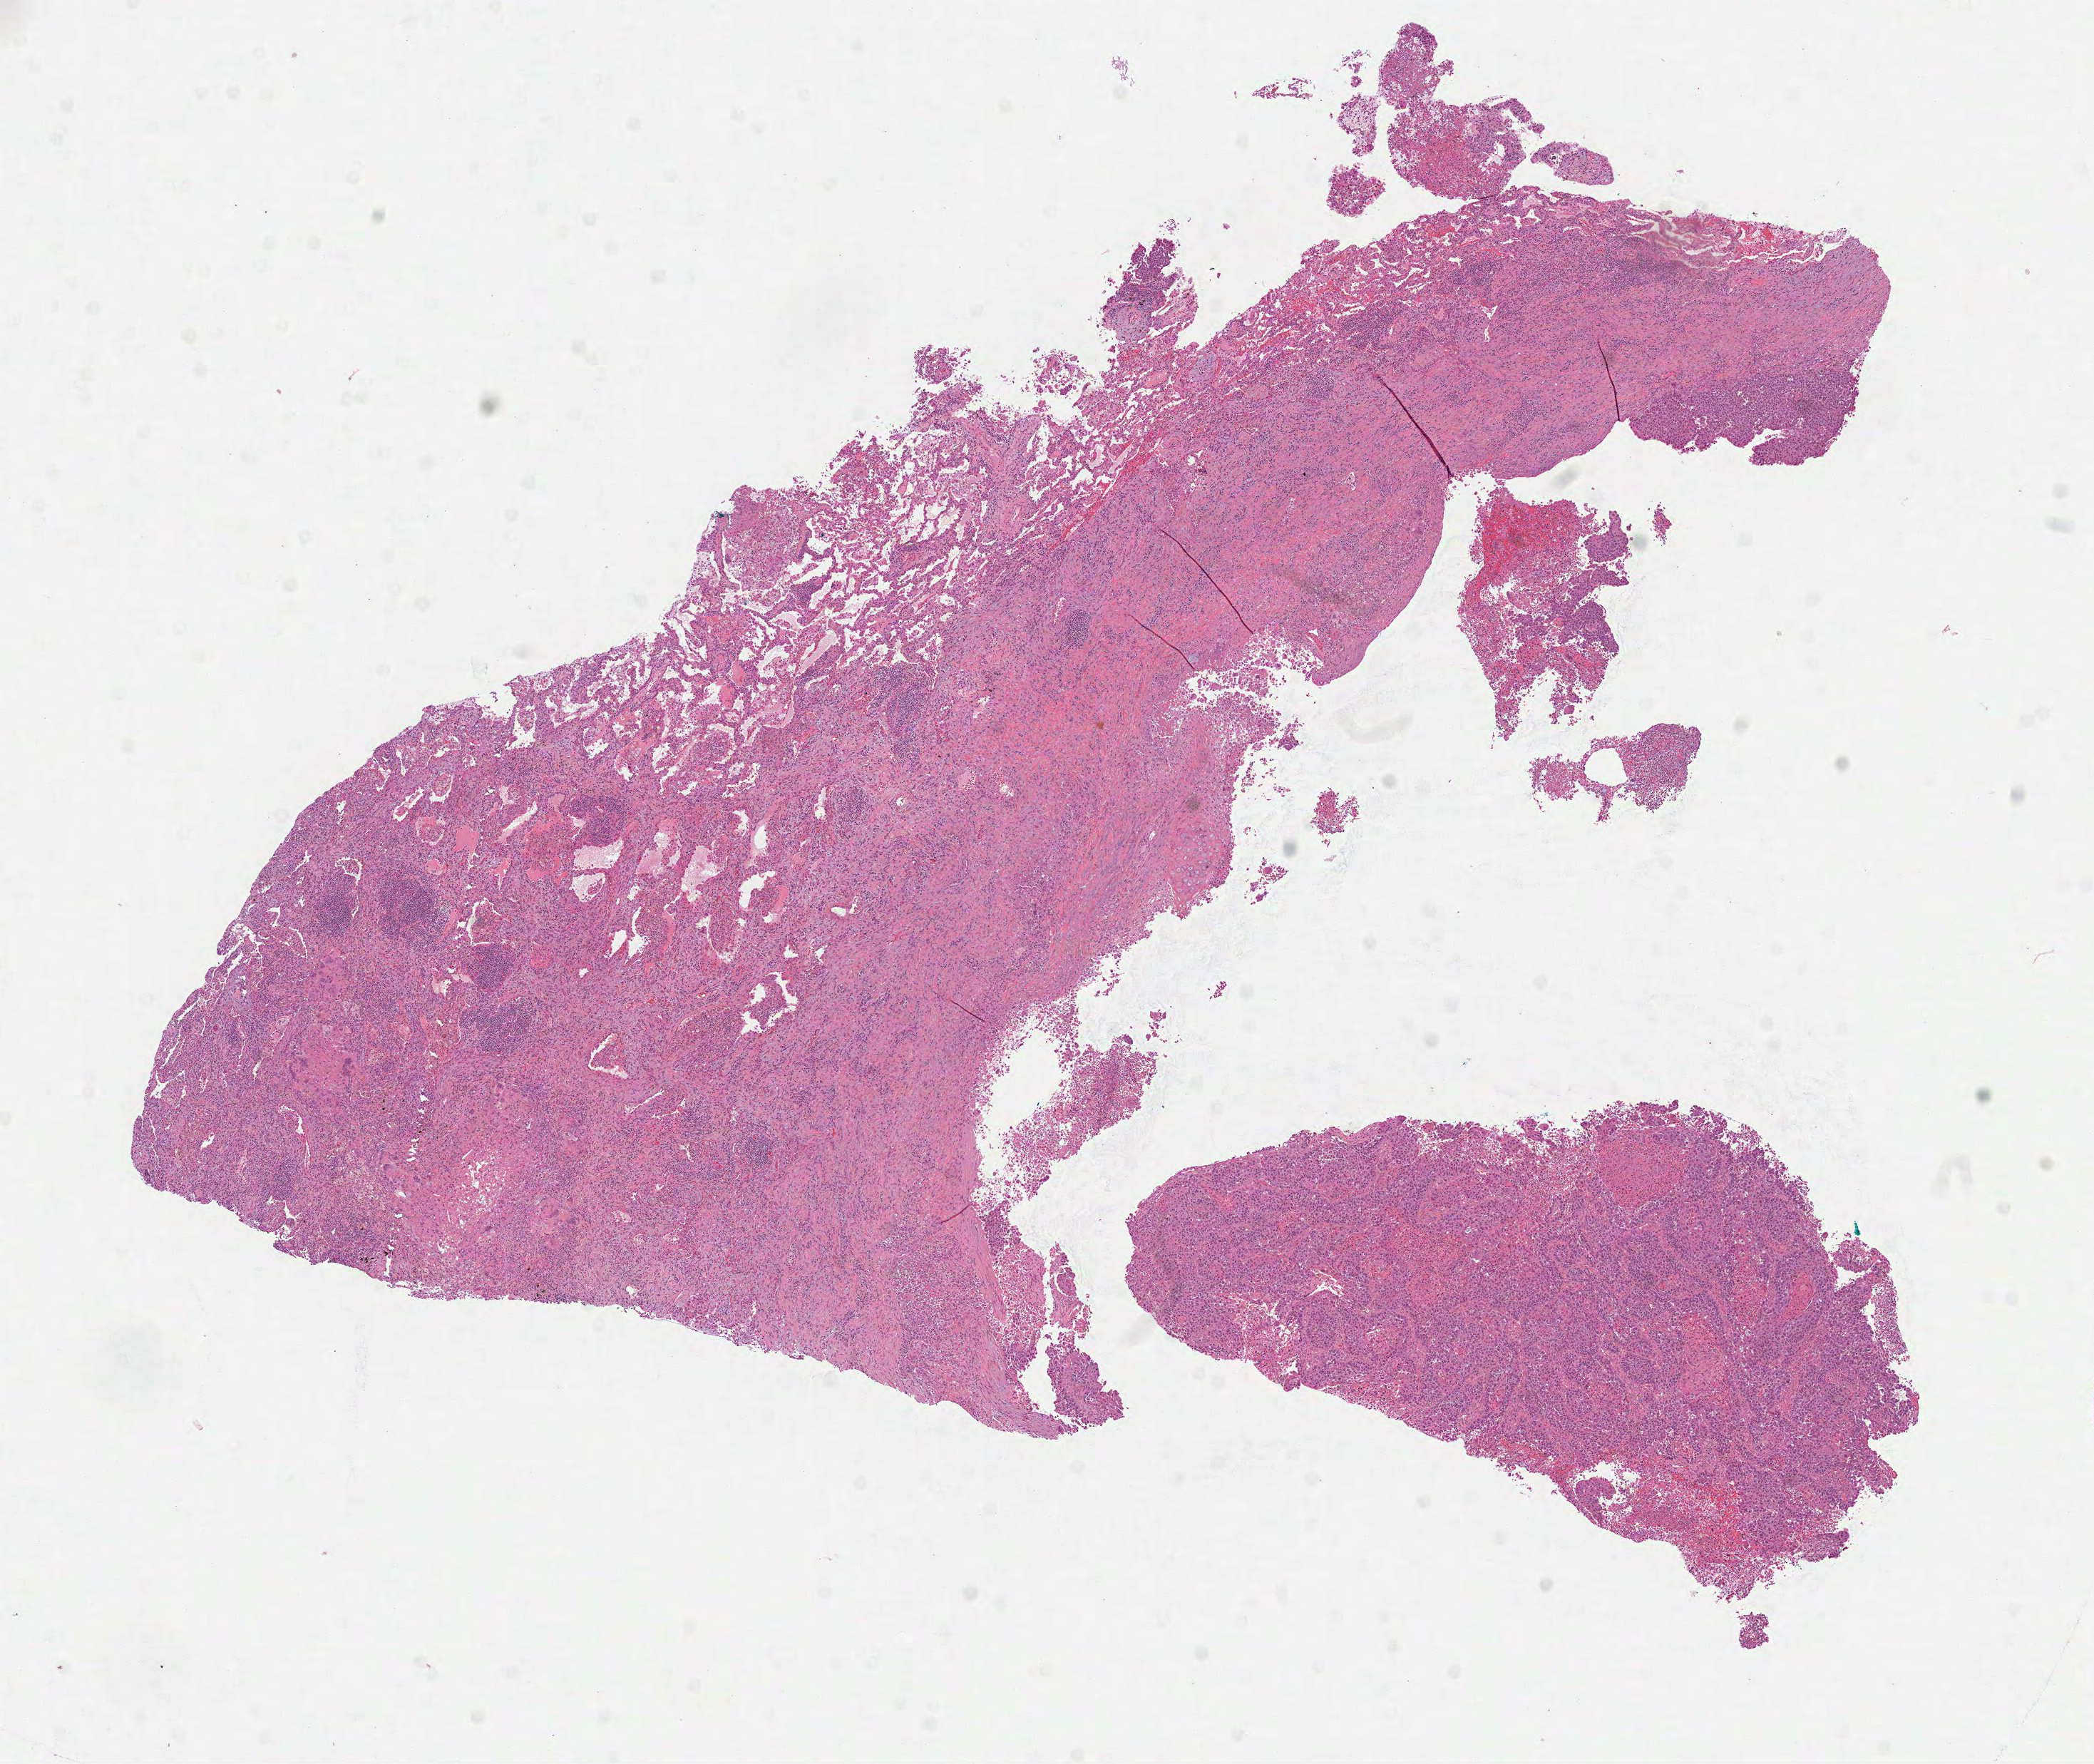
Hematoxylin and eosin (H&E) stained whole-slide image — low-resolution overview of the scanned area, about 11.8 x 10.0 mm (slide scanned at 40x). Formalin-fixed paraffin-embedded (FFPE) diagnostic section. Lung, primary tumour sample. Male, age 61 years at initial diagnosis.
• TNM: T3 N1 M0
• histologic diagnosis: Squamous cell carcinoma, NOS (upper lobe, lung)
• AJCC pathologic stage: IIIA